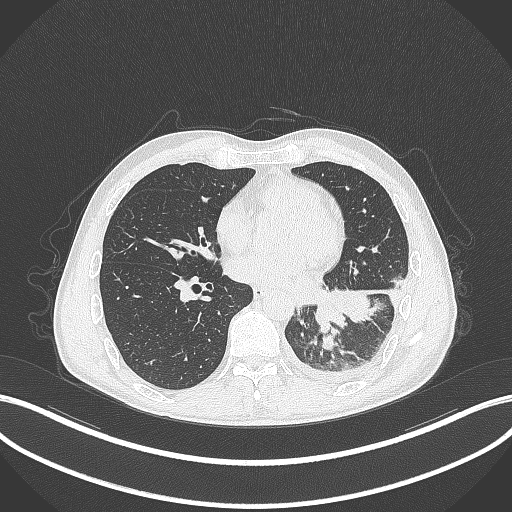
Chest CT, one axial slice. Slice 130 of 295 in the series (ordered by position). Reconstruction kernel B70f. Lung window (W 1500 / L -600 HU). 1 mm slice thickness. 512 × 512 image matrix, field of view 400 × 400 mm. Male patient, age 47 years. Case-level facts recorded for this patient, not image findings: clinical TNM (as recorded): T3 N1 M1c.
Annotated regions visible in this slice (rectangle marked by the reading radiologist):
- lung tumour (recorded histology: small cell carcinoma): bounding box <310,289,347,329> (left, top, right, bottom; pixels)